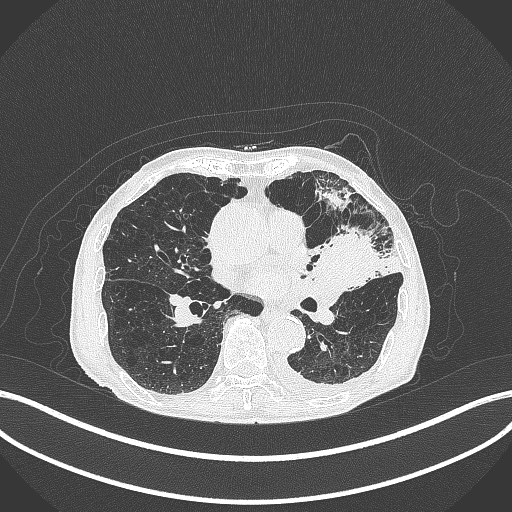
Chest CT, one axial slice; position 188 of 385 along the scan axis; reconstruction kernel B70f; 120 kVp; lung window (W 1500 / L -600 HU); 1 mm slice thickness; 512 × 512 image matrix. Patient: male, 90 years or older. Case-level facts recorded for this patient, not image findings: clinical TNM (as recorded): T2b N1 M0.
Outlined on this slice (rectangle marked by the reading radiologist):
- lung tumour (recorded histology: squamous cell carcinoma): bounding box [x1, y1, x2, y2] px = [314, 229, 380, 291]